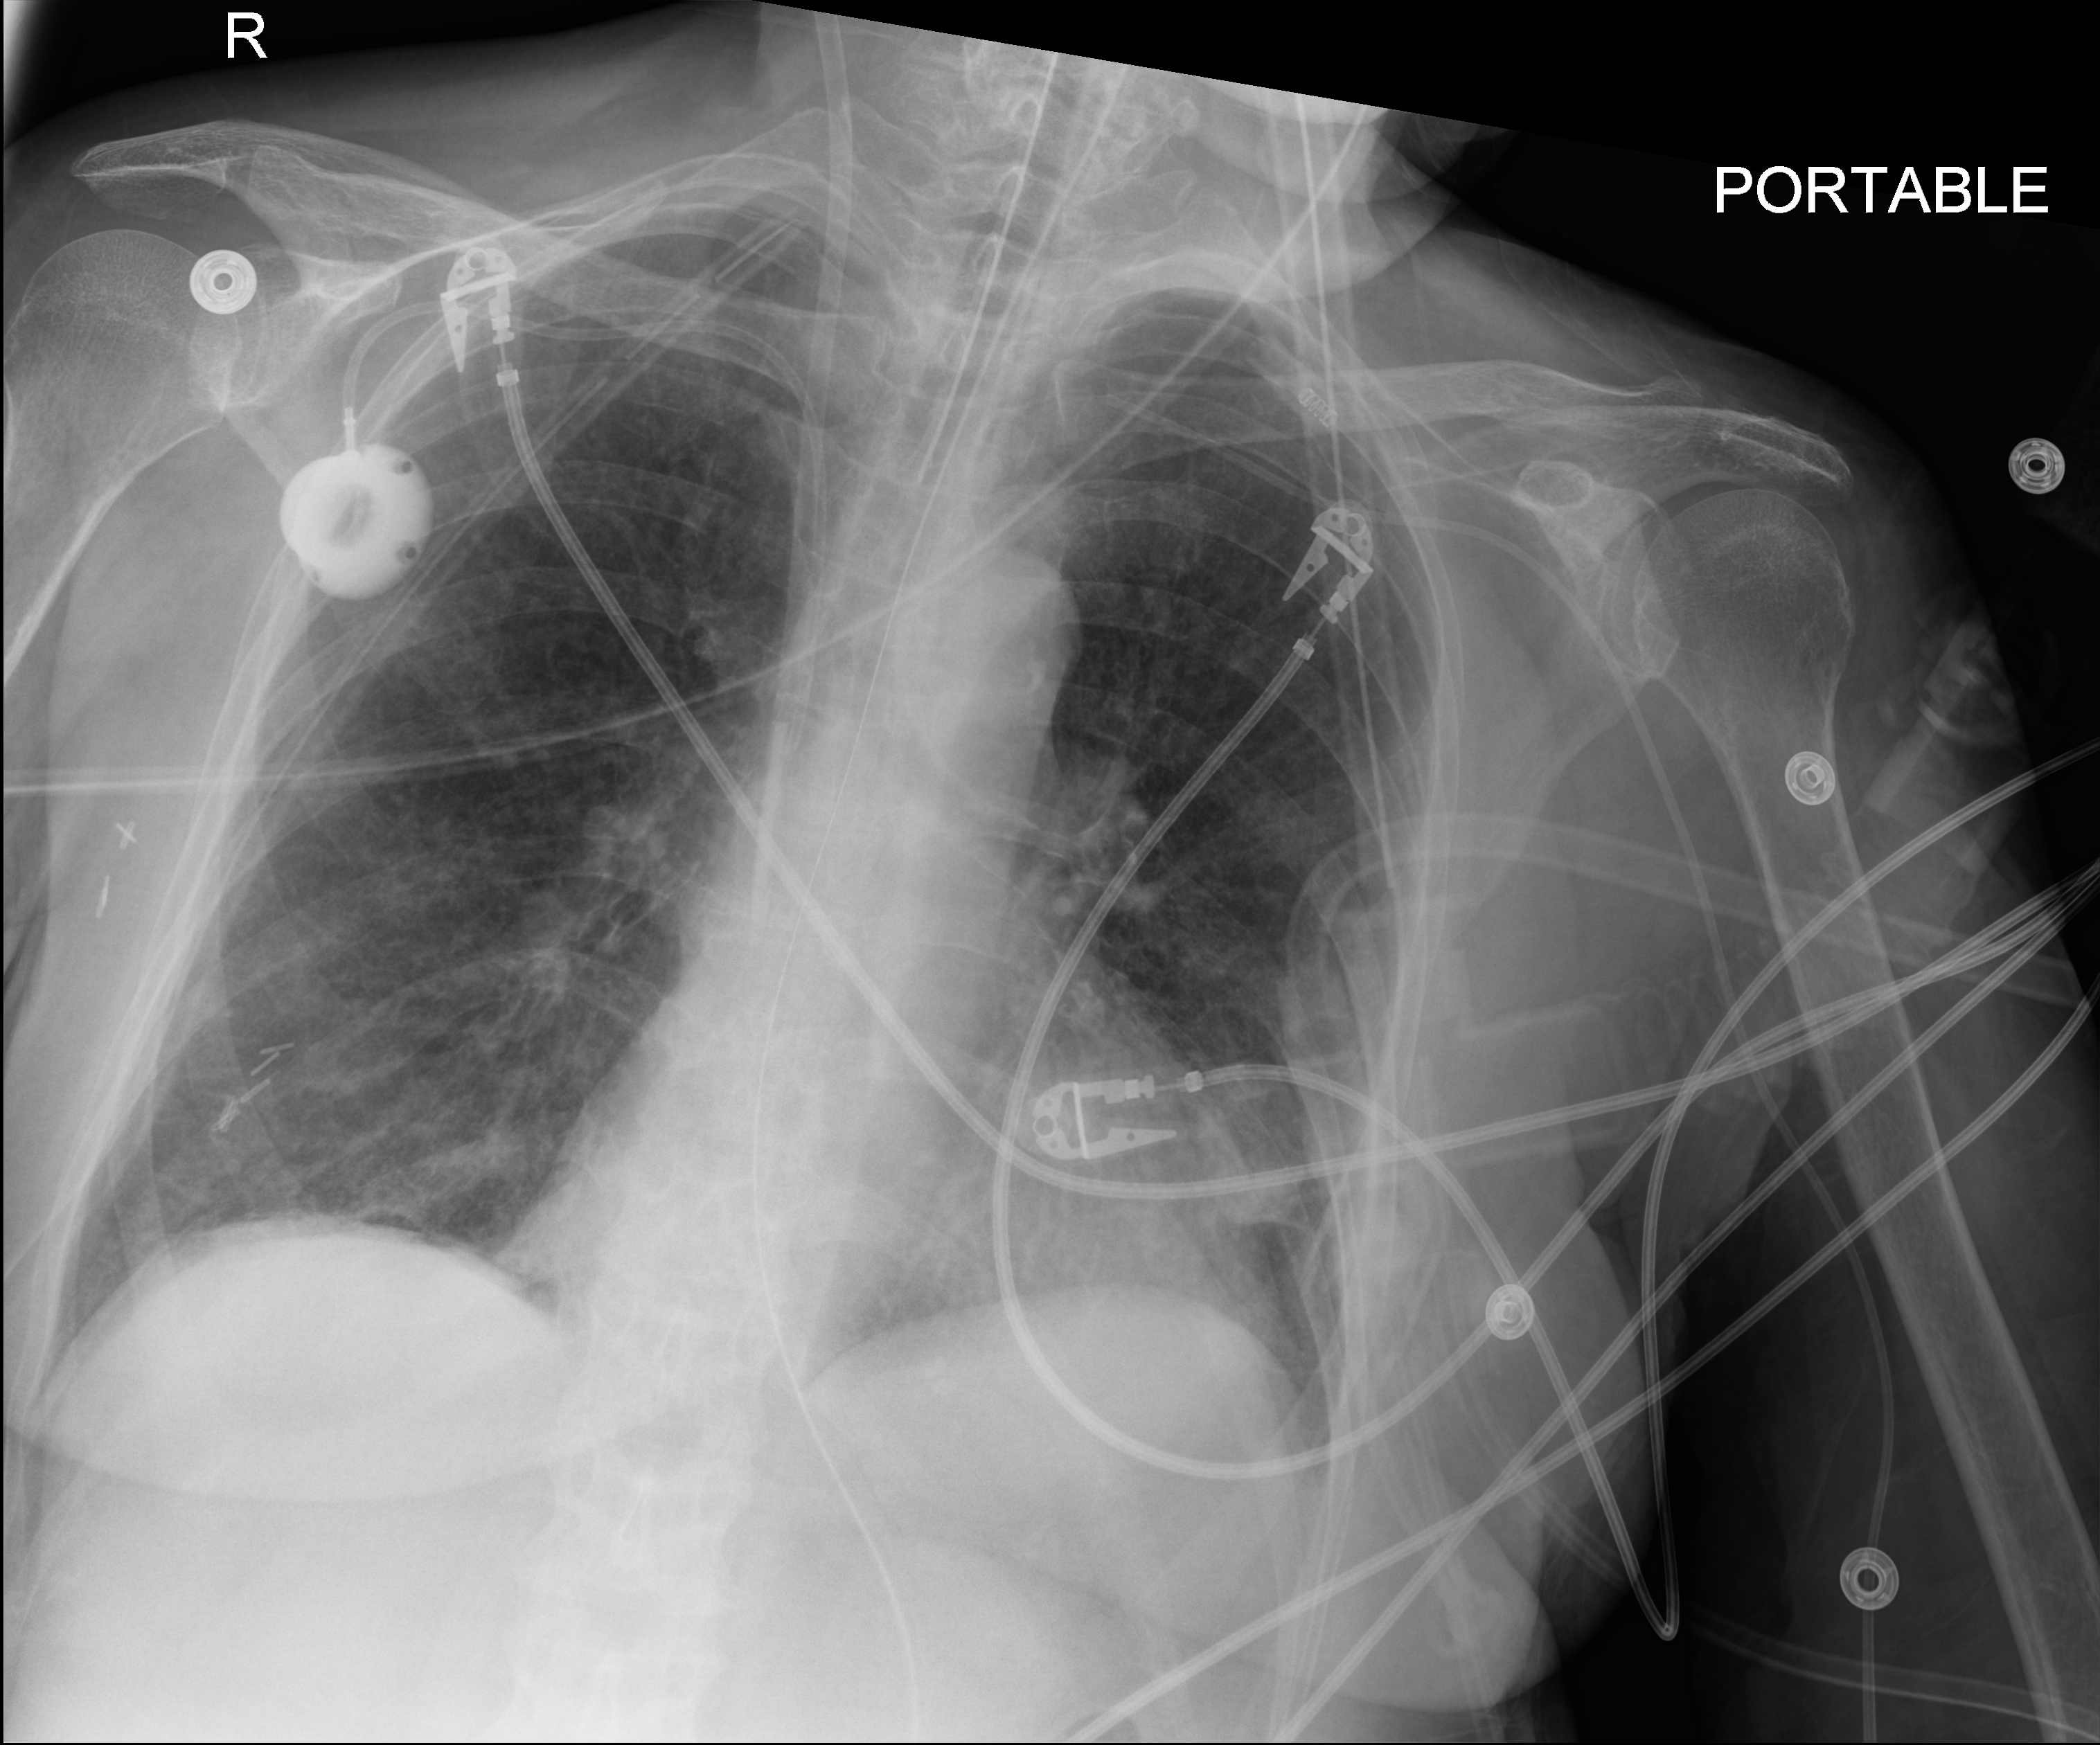
Chest X-ray (portable); anteroposterior (AP) projection. Patient hospitalised with COVID-19; female, aged 60–74 years.
Admission-level facts for this patient (not findings on this image; timing relative to this image not recorded):
- admitted to intensive care during this hospital stay: yes
- mechanically ventilated during this hospital stay: yes